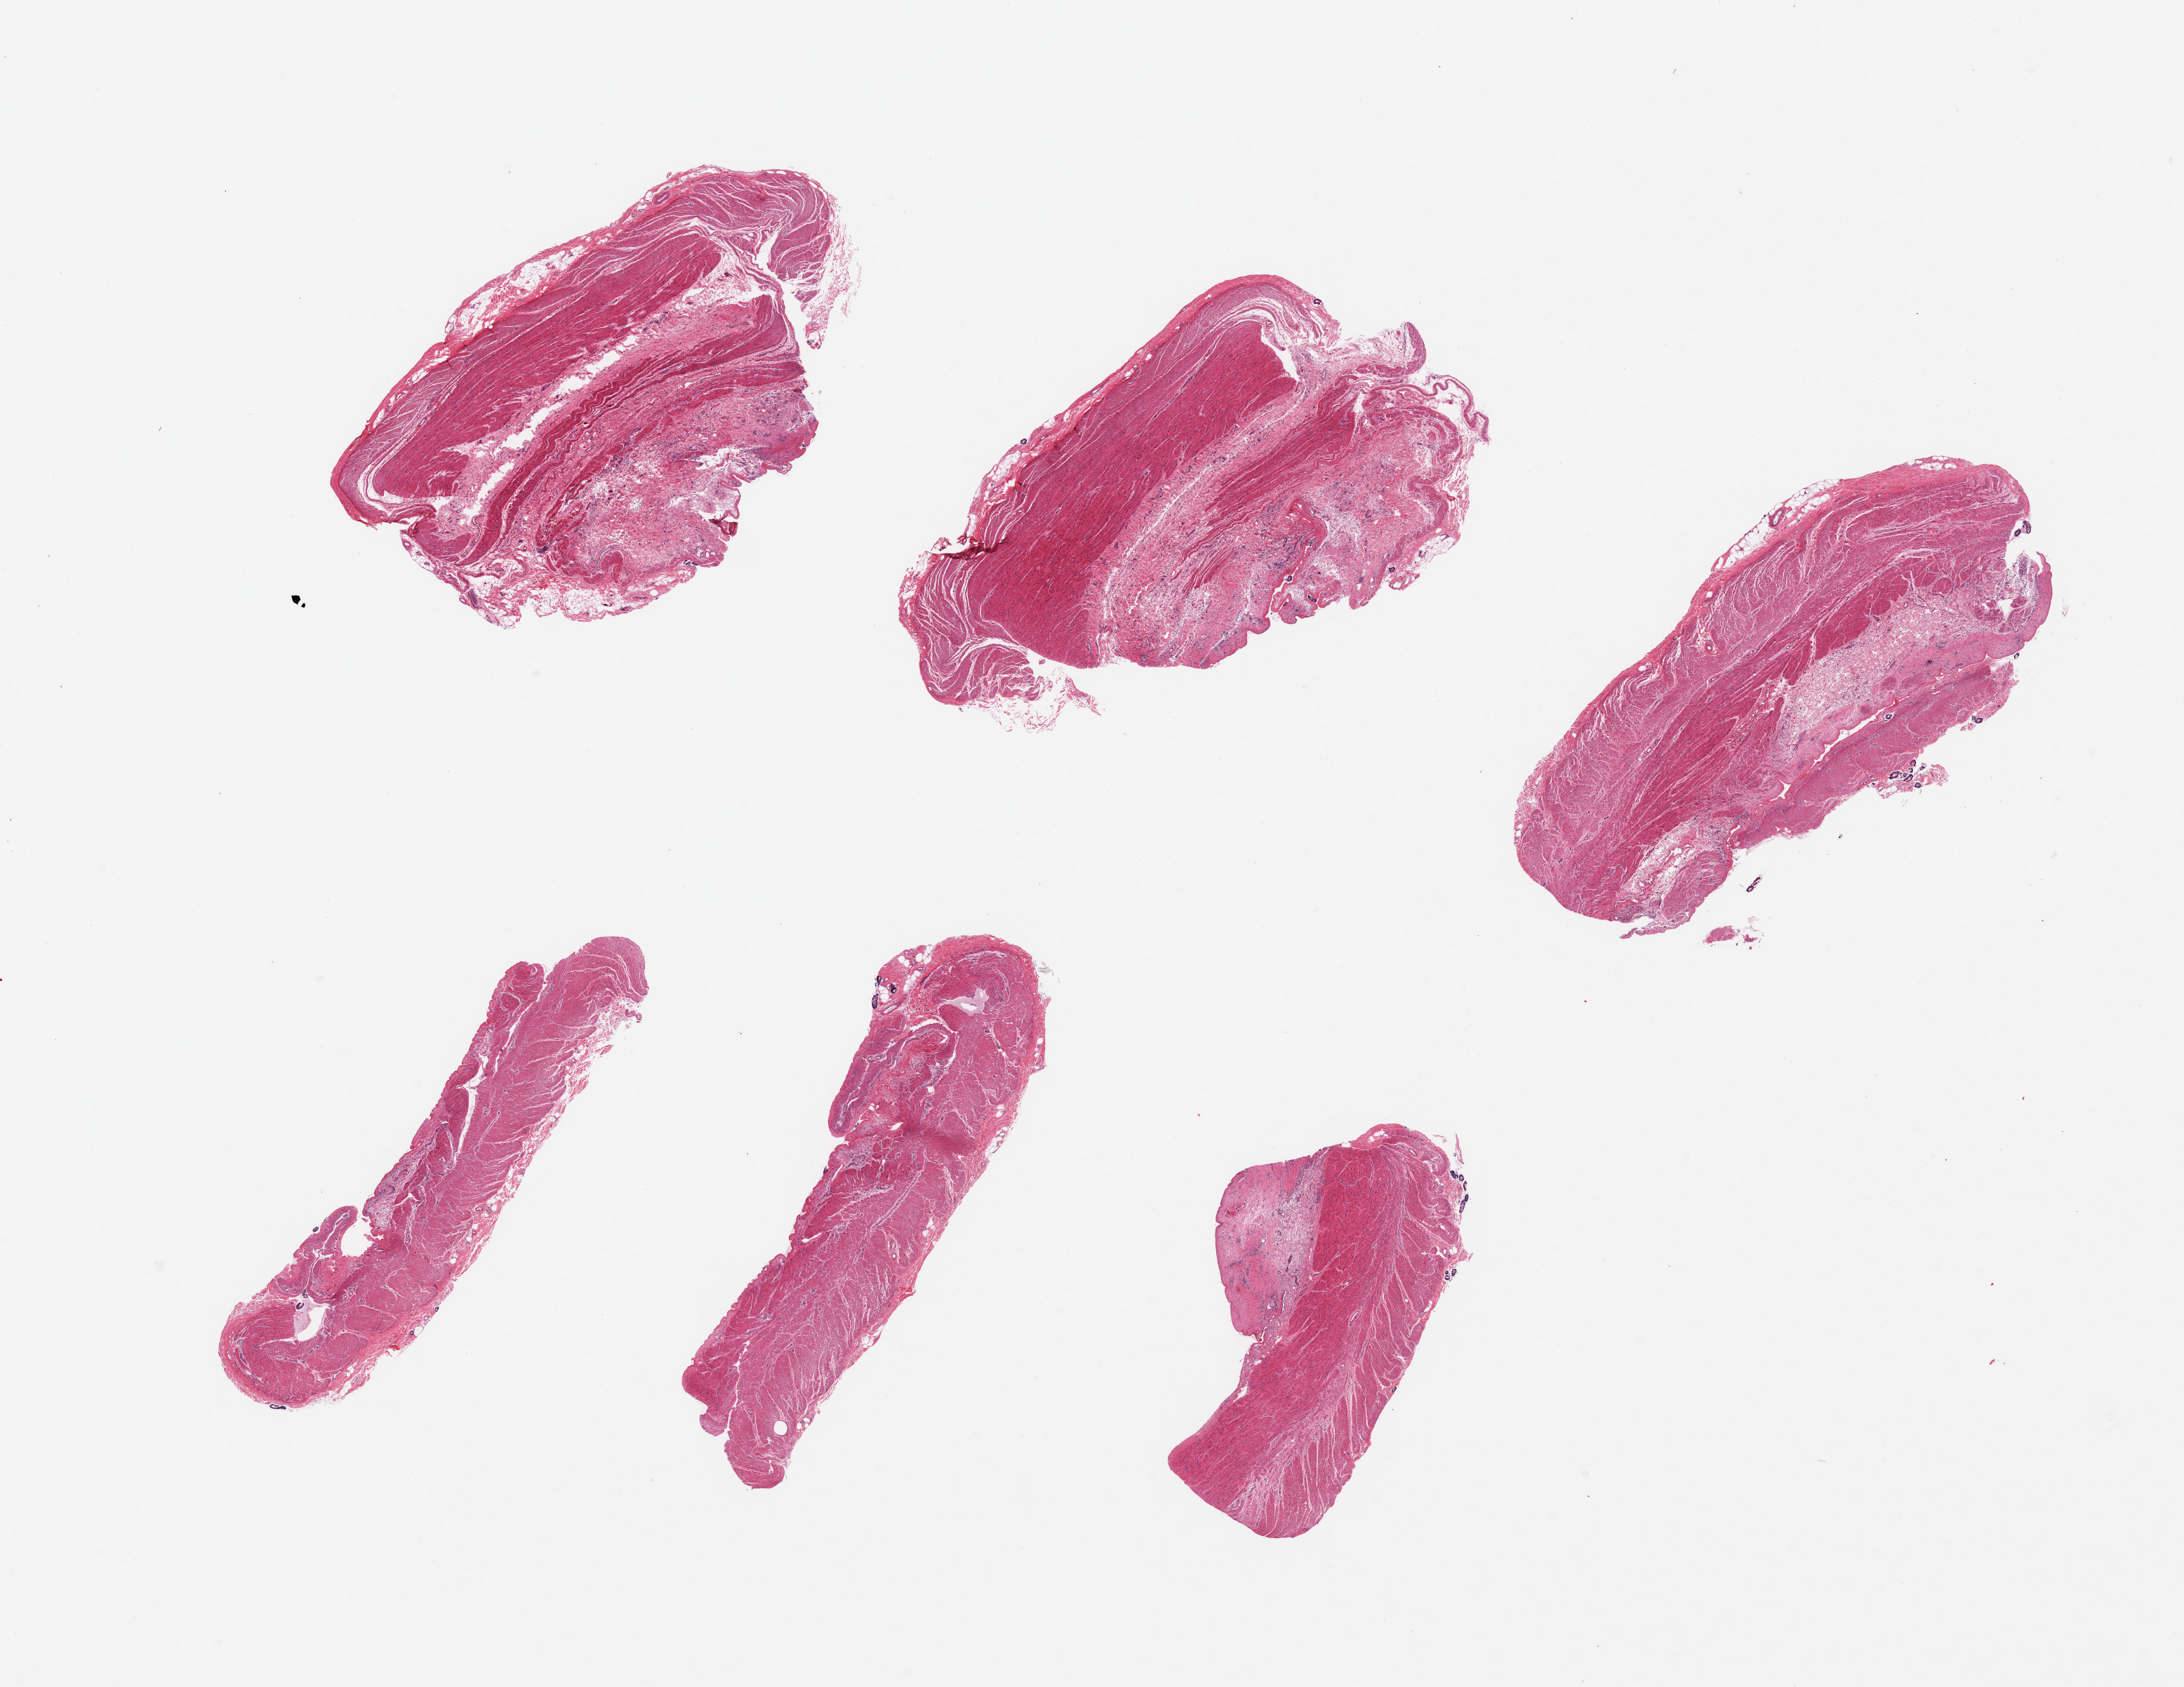
Digitized hematoxylin and eosin (H&E)-stained section — low-resolution overview of the scanned area, about 24.6 x 19.0 mm. PAXgene-fixed, paraffin-embedded tissue. Section of sigmoid colon (target tissue). Donor tissue sample. Donor sex: female.
Review note (as recorded): 6 pieces; target muscularis with attached serosa.